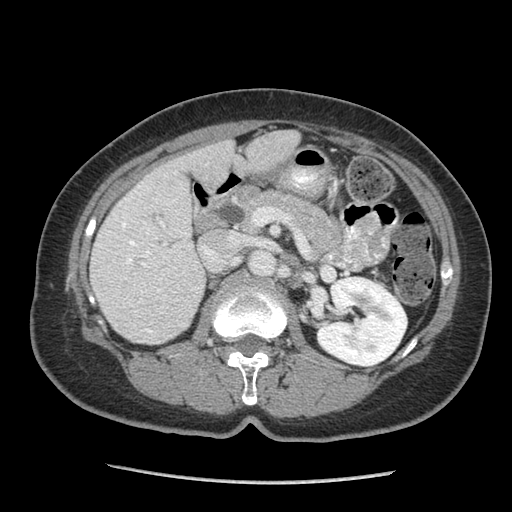
Contrast-enhanced abdominal CT (liver protocol), one axial slice; position 37 of 105 along the scan axis; reconstruction kernel STANDARD; 140 kVp; soft-tissue window (W 400 / L 40 HU); 2.5 mm slice thickness; 512 × 512 image matrix. From the clinical record (not read from this slice): diagnosis: hepatocellular carcinoma (patient treated with transarterial chemoembolisation; whether this scan precedes or follows treatment is not stated here); TNM stage (as recorded): Stage-I; Child-Pugh class: A; tumour differentiation: moderately differentiated; tumour nodularity: uninodular.
Structures marked on this image (semi-automatically segmented with operator editing):
- liver parenchyma outside the tumour (the mass and vessels are separate outlines, so this box may not span the whole liver): bounding box (x1, y1, x2, y2) in pixels: (90, 130, 300, 344)
- liver vessels: (107, 172, 176, 333)